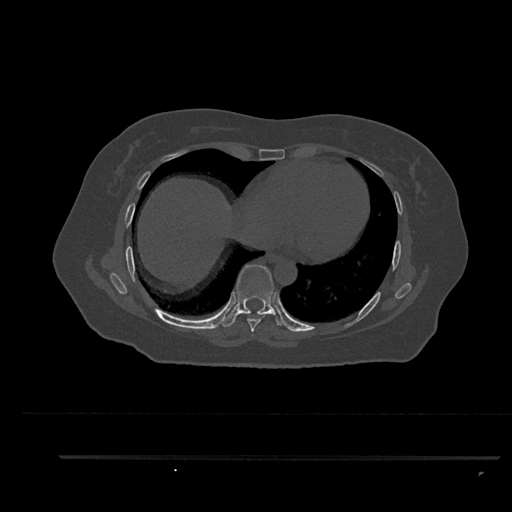
CT including the spine, one axial slice. Position 480 of 797 along the scan axis. Reconstruction kernel Br40s/3. 120 kVp. Bone window (W 1800 / L 400 HU). 0.5 mm slice thickness. 512 × 512 image matrix. Patient: female, 44 years. From the clinical record (not read from this slice): primary cancer: renal.
Annotated regions visible in this slice (semi-automatically segmented with operator editing):
- T7 vertebra: box from (x=242, y=313) to (x=266, y=332) px
- T8 vertebra: (x=222, y=264)–(x=285, y=327)